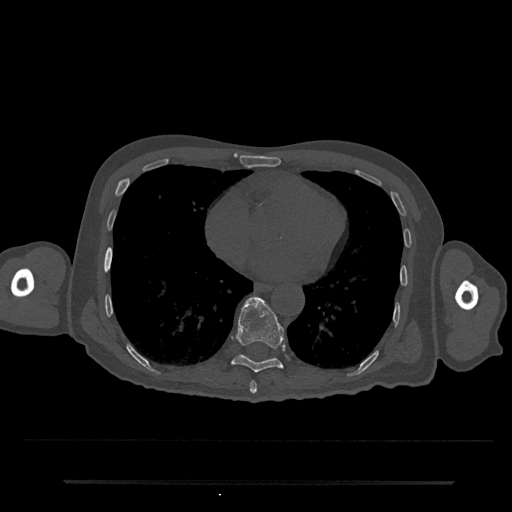
CT including the spine, one axial slice; position 362 of 797 along the scan axis; reconstruction kernel Br40s/3; bone window (W 1800 / L 400 HU); 0.5 mm slice thickness; 512 × 512 image matrix, field of view 427 × 427 mm. Patient: male, 74 years. From the clinical record (not read from this slice): primary cancer: prostate.
Annotated regions visible in this slice (semi-automatically segmented with operator editing):
- T8 vertebra: bounding box [x1, y1, x2, y2] px = [250, 381, 257, 394]
- T9 vertebra: [231, 296, 284, 373]